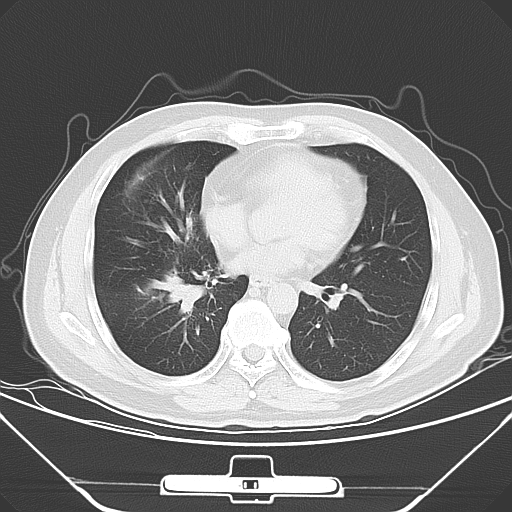
Chest CT, one axial slice; slice 24 of 56 in the series (ordered by position); 120 kVp; lung window (W 1500 / L -600 HU); 5 mm slice thickness; 512 × 512 image matrix, field of view 371 × 371 mm. Patient: male, 48 years. From the clinical record (not read from this slice): clinical TNM (as recorded): T1a N1 M1c.
Annotated regions visible in this slice (bounding box drawn by a radiologist):
- lung tumour (recorded histology: adenocarcinoma): box from (x=156, y=273) to (x=204, y=323) px